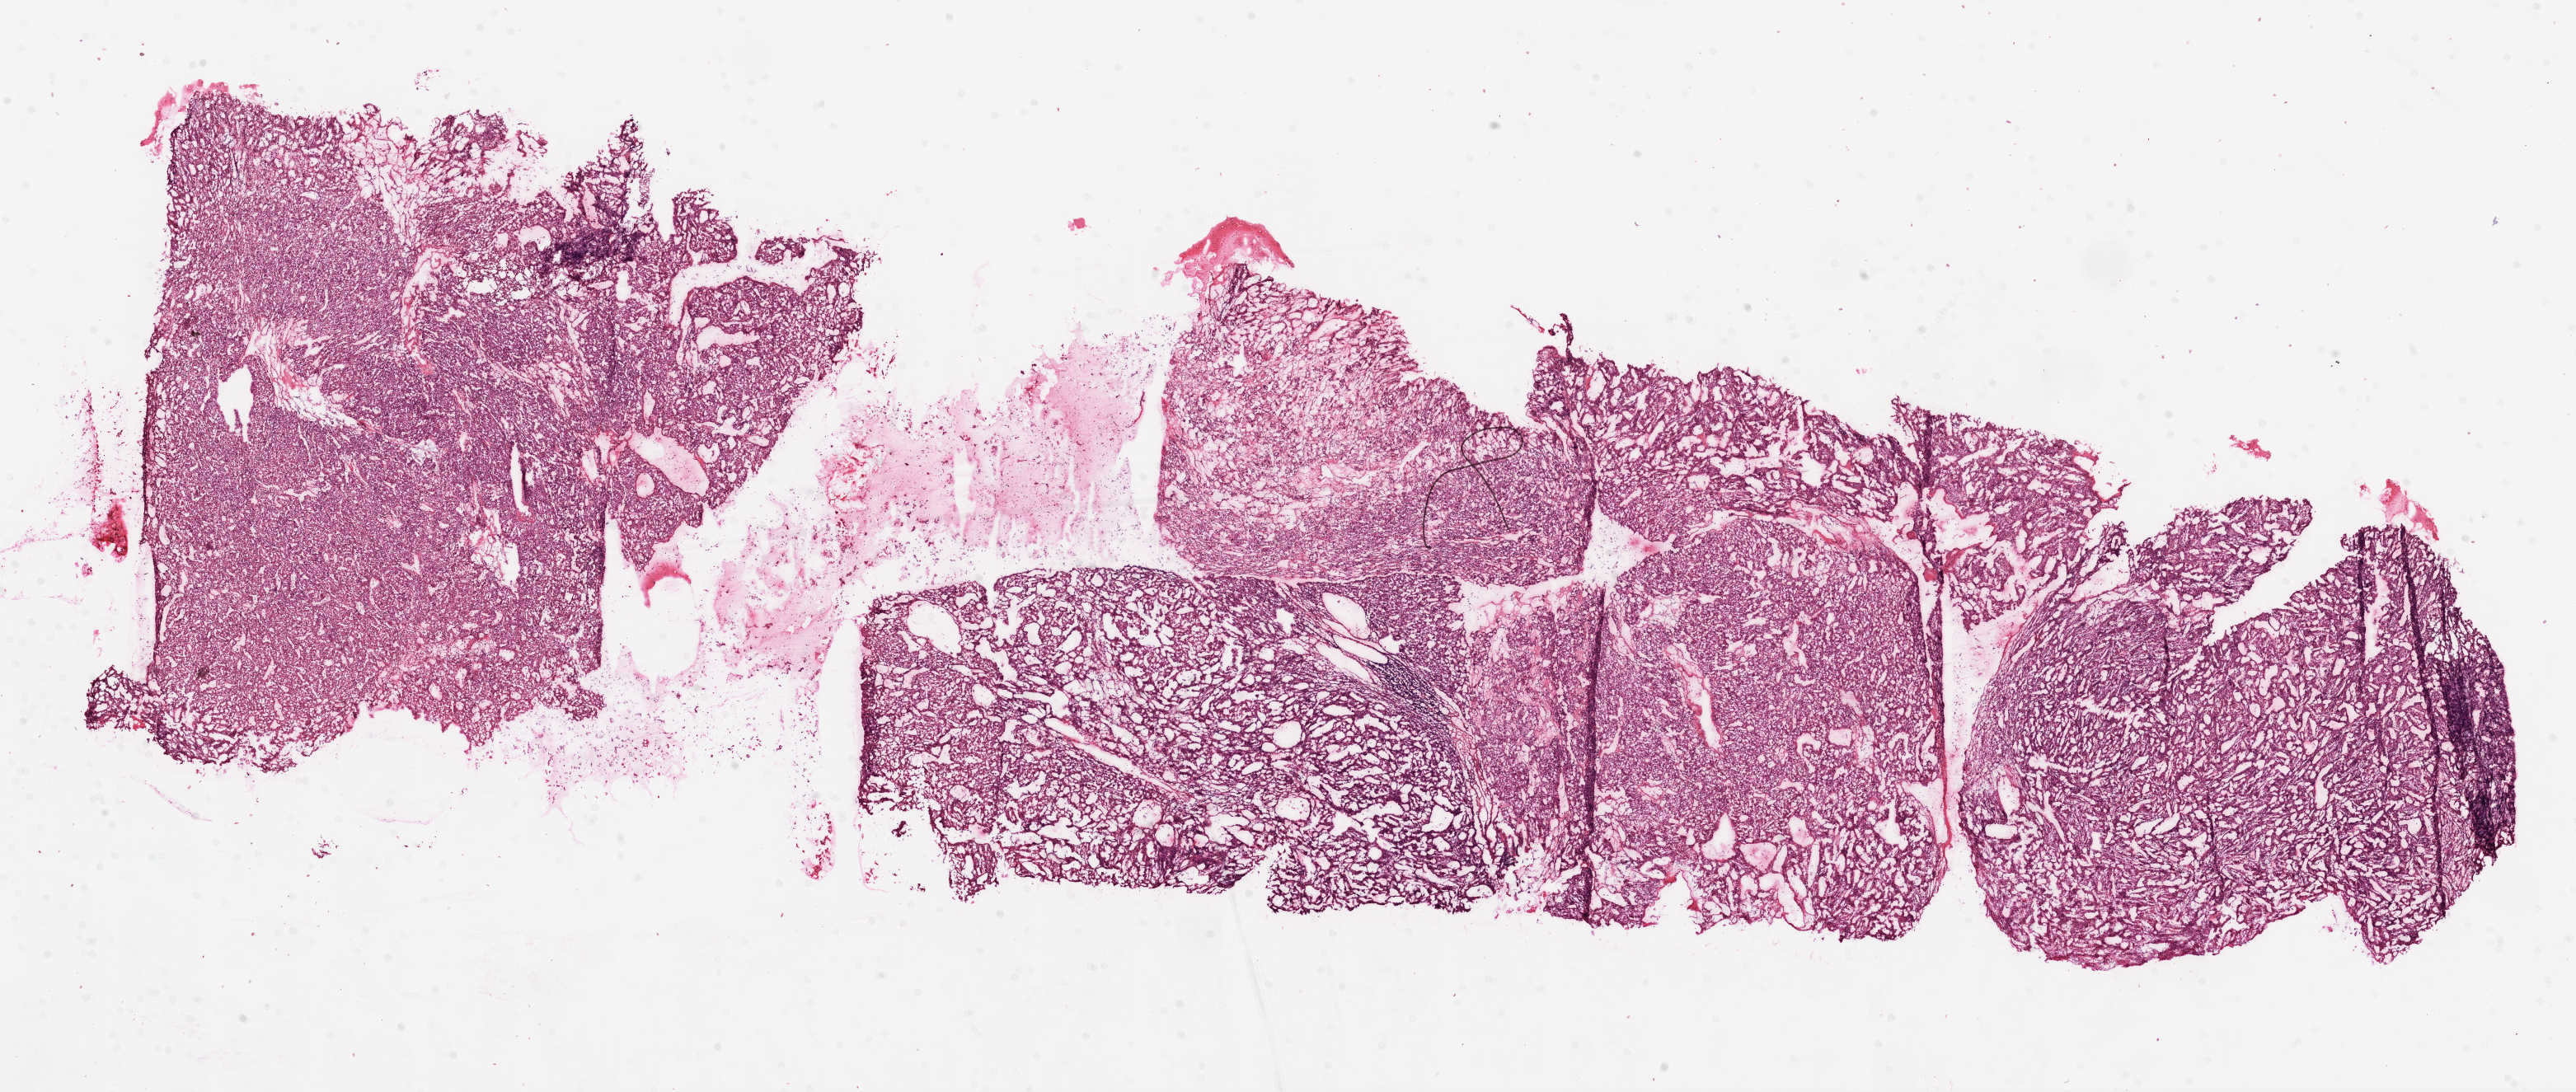
H&E whole-slide image — a low-resolution overview of the entire scanned area, about 25.1 x 10.6 mm (slide scanned at 20x); frozen section from the top of the tissue portion; primary tumour sample from the kidney. Patient: male, age at initial diagnosis 57 years.
Histologic diagnosis: Clear cell adenocarcinoma, NOS.